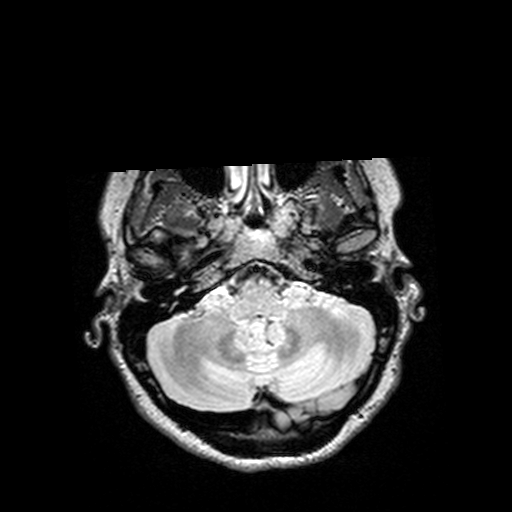
Brain MRI from a brain-tumour surgery series, one axial slice. Slice 114 of 144 in the series (ordered by position). T2 FLAIR. 1 mm slice thickness. 512 × 512 image matrix, field of view 250 × 250 mm. From the clinical record (not read from this slice): histopathology: Astrocytoma; WHO grade: 3; IDH mutation: yes.
Annotated regions visible in this slice (outlined manually by an expert reader):
- tumour: box from (x=173, y=243) to (x=187, y=253) px